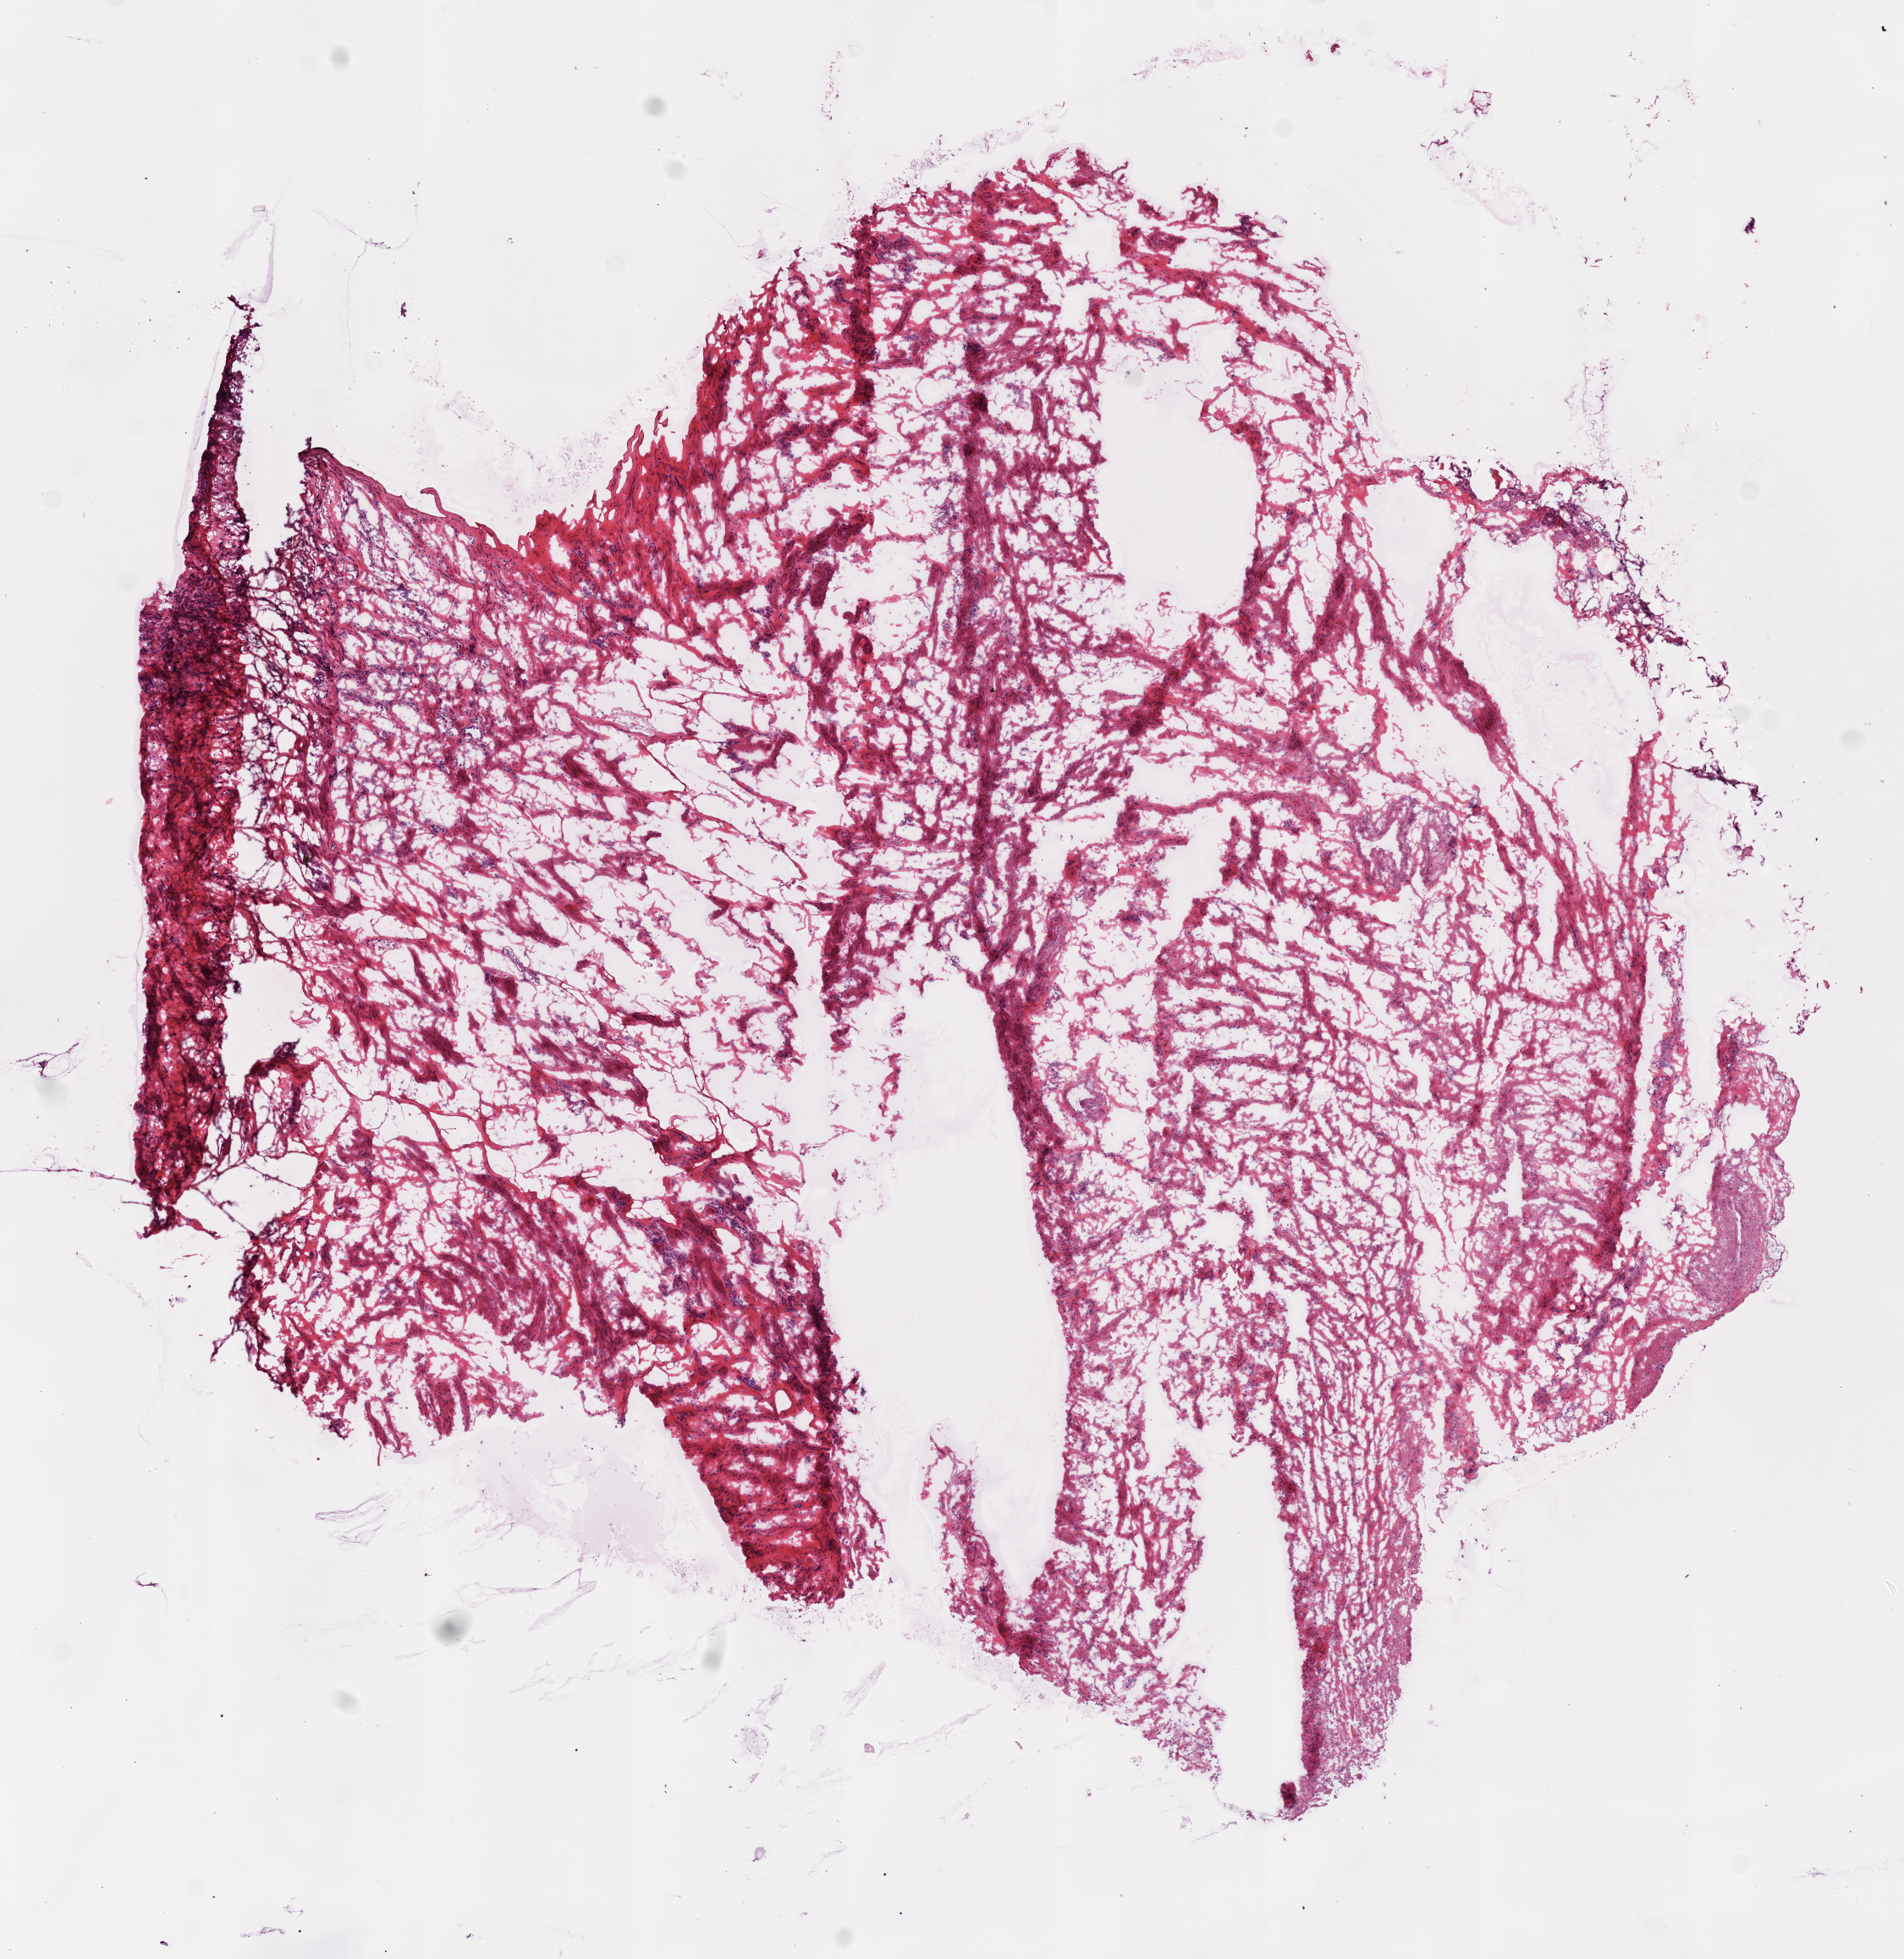
Digitized H&E tissue section (whole slide), whole scanned area (about 9.0 x 9.3 mm) shown as a low-resolution overview, frozen section, ovary, solid tissue normal (non-tumour tissue) sample. Female patient; age at initial diagnosis 57 years.
This section: solid tissue normal sample (biorepository sample class). Patient diagnosis: Serous cystadenocarcinoma, NOS.